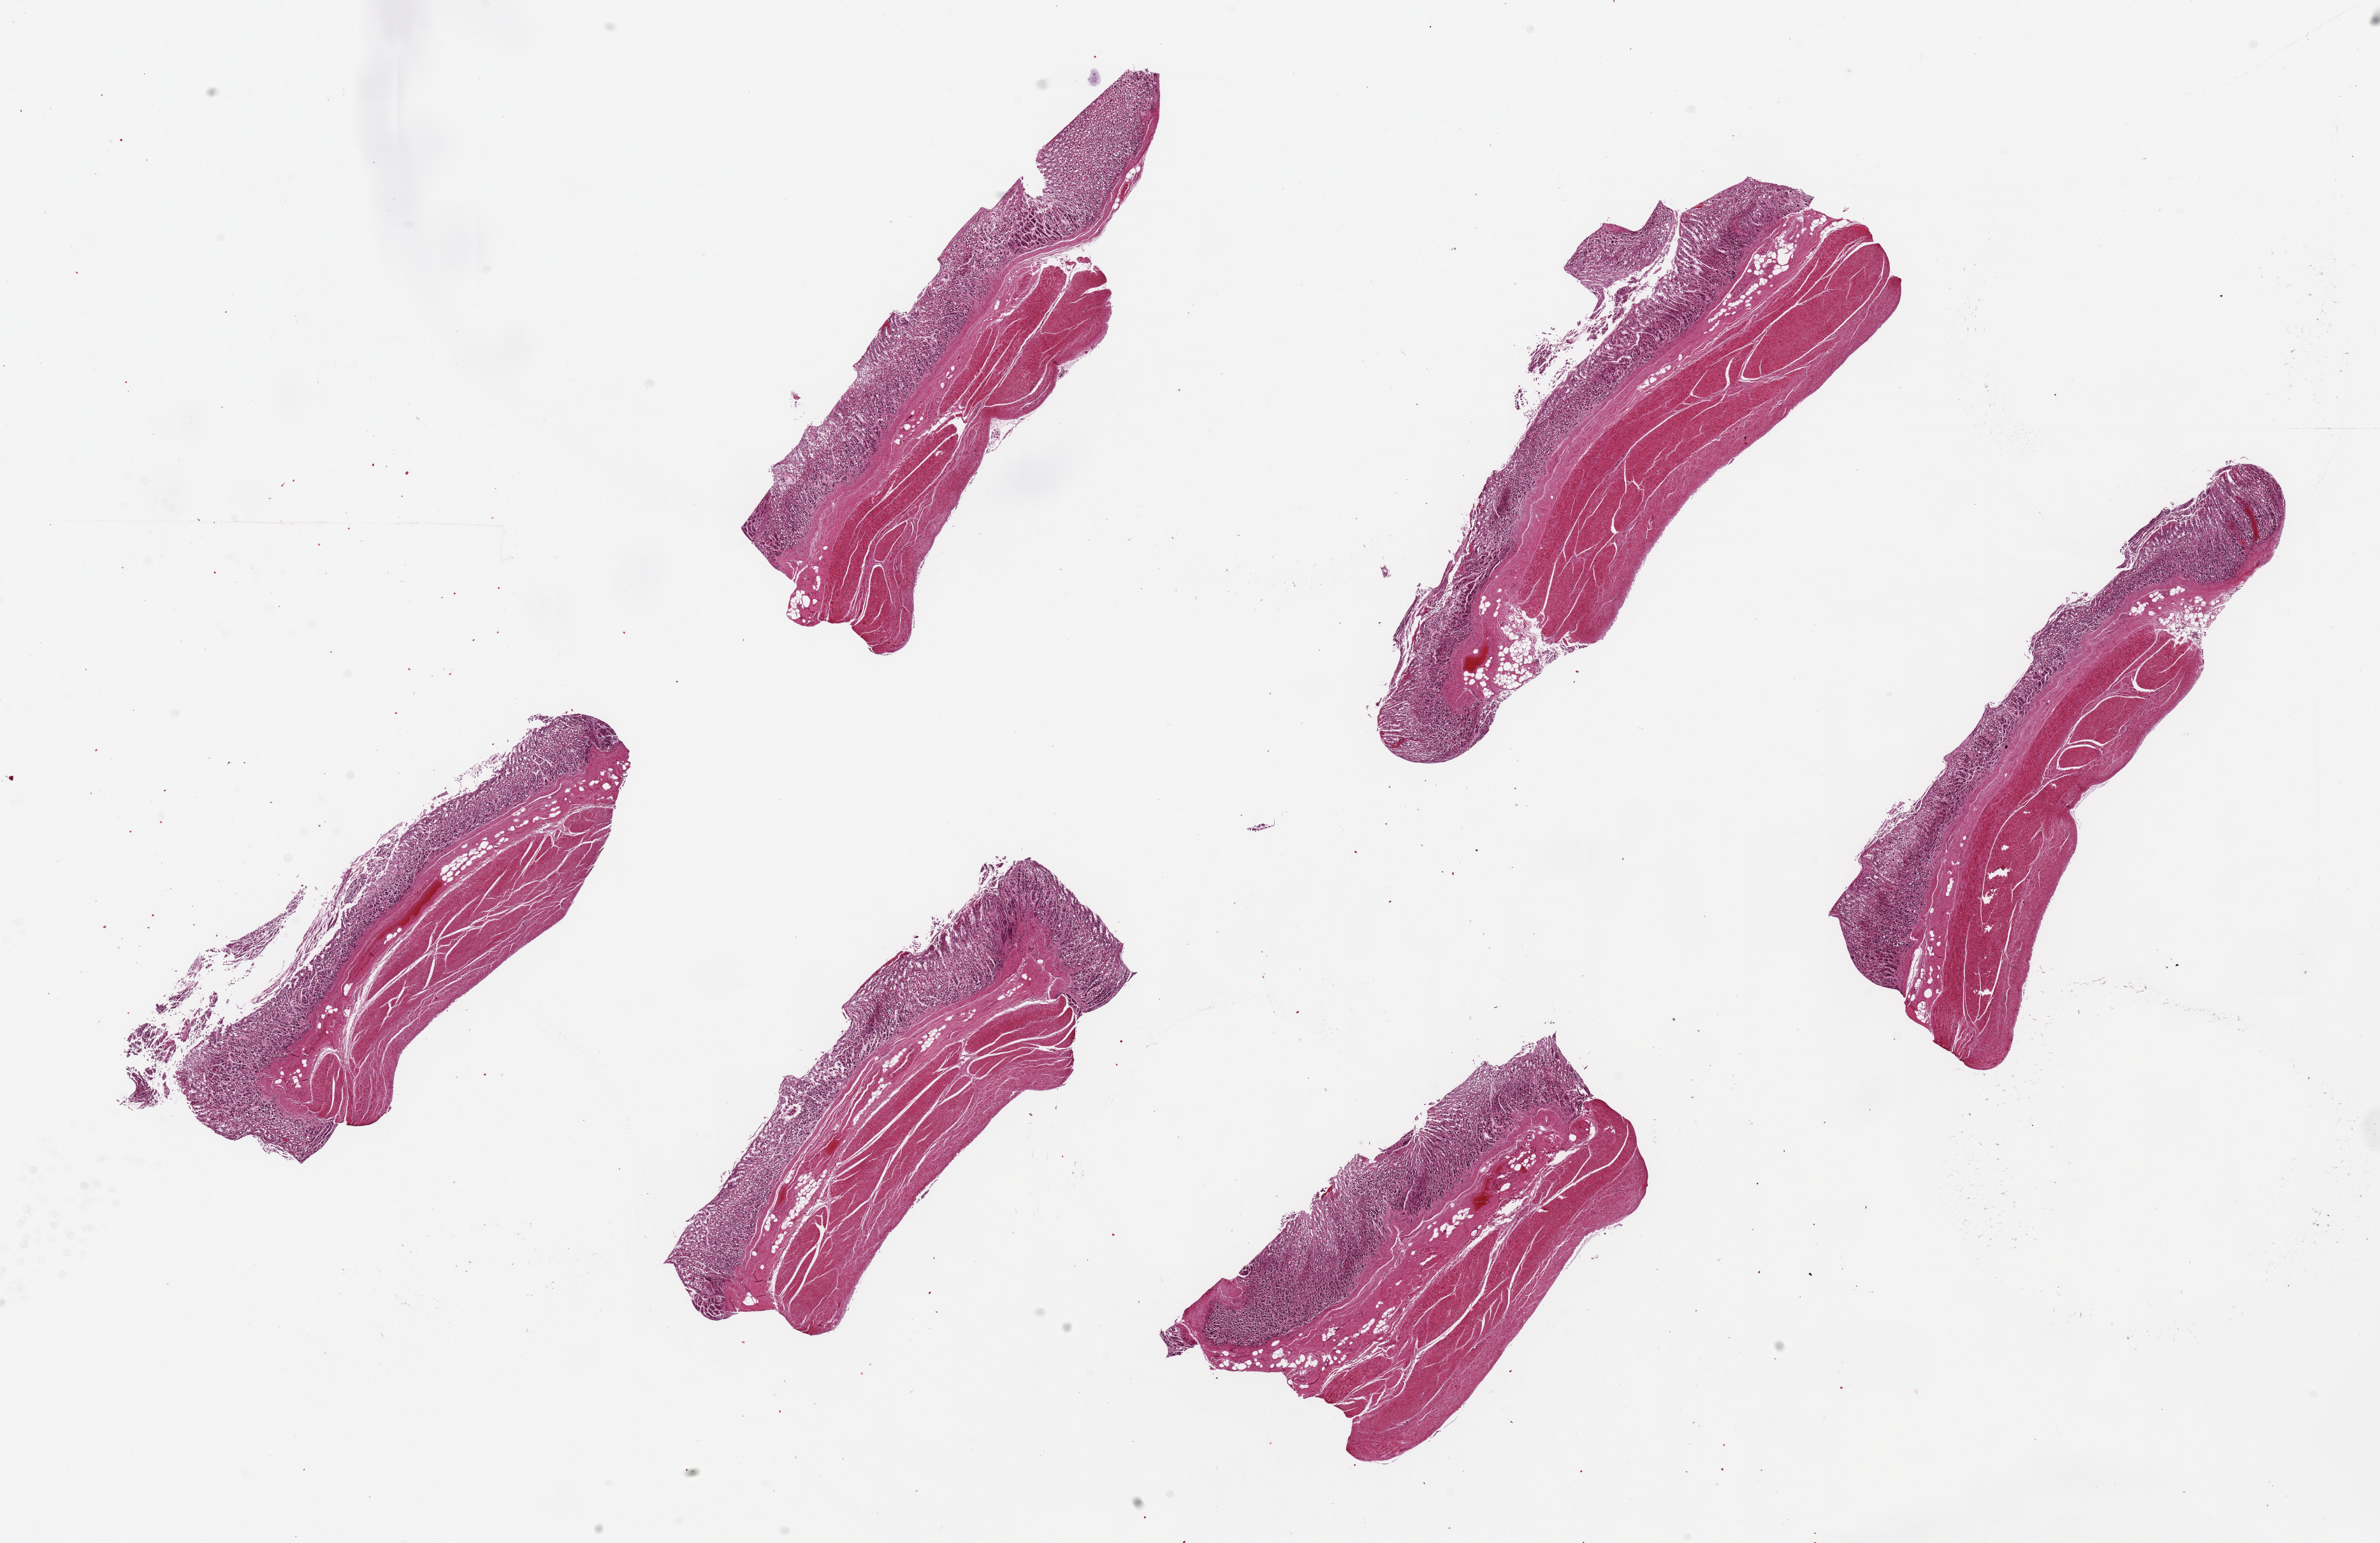
Haematoxylin and eosin whole-slide image, brightfield — whole scanned area (about 29.5 x 19.1 mm, from a 20x scan) shown as a low-resolution overview, PAXgene-fixed, paraffin-embedded tissue, section of stomach (target tissue), donor tissue sample. Donor sex: male.
Review note (as recorded): 6 pieces, up to 9x3mm; Well sampled mucosa (3) and muscle (2).